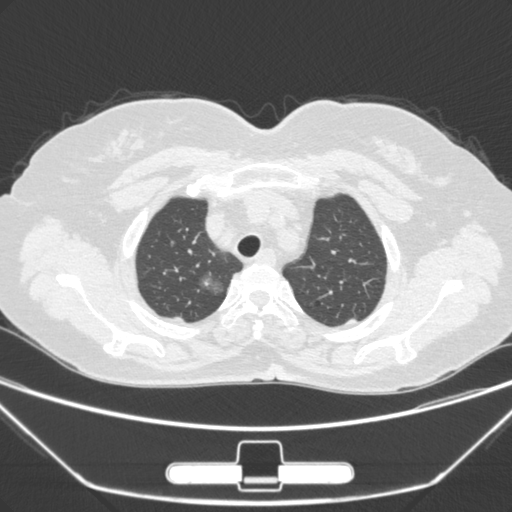
Chest CT, one axial slice. Slice 232 of 275 in the series (ordered by position). Lung window (W 1500 / L -600 HU). 512 × 512 image matrix. Female patient, age 63 years. Case-level facts recorded for this patient, not image findings: clinical TNM (as recorded): T1a N0 M0; histopathological grade: G1.
Structures marked on this image (rectangle marked by the reading radiologist):
- lung tumour (recorded histology: adenocarcinoma): bounding box <194,272,226,306> (left, top, right, bottom; pixels)